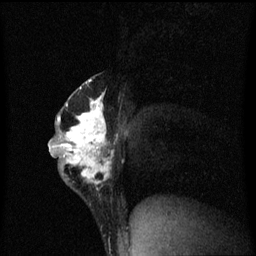
Breast MRI (dynamic contrast-enhanced), one sagittal slice. Position 35 of 60 along the scan axis. Dynamic contrast-enhanced series, image 2 of 3 at this slice position (ordered by acquisition). 1.5 T. TE 4.2 ms, TR 8.4 ms. 256 × 256 image matrix, field of view 200 × 200 mm. Female patient, age 40 years.
Outlined on this slice (semi-automatic segmentation, software-assisted and operator-edited):
- analysis volume of interest (the breast-tissue region the enhancement analysis was run in; not a lesion): box from (x=50, y=74) to (x=115, y=201) px
- tumour enhancement mask (voxels above the 70 % enhancement threshold inside the analysis volume of interest): (x=50, y=80)–(x=114, y=191)